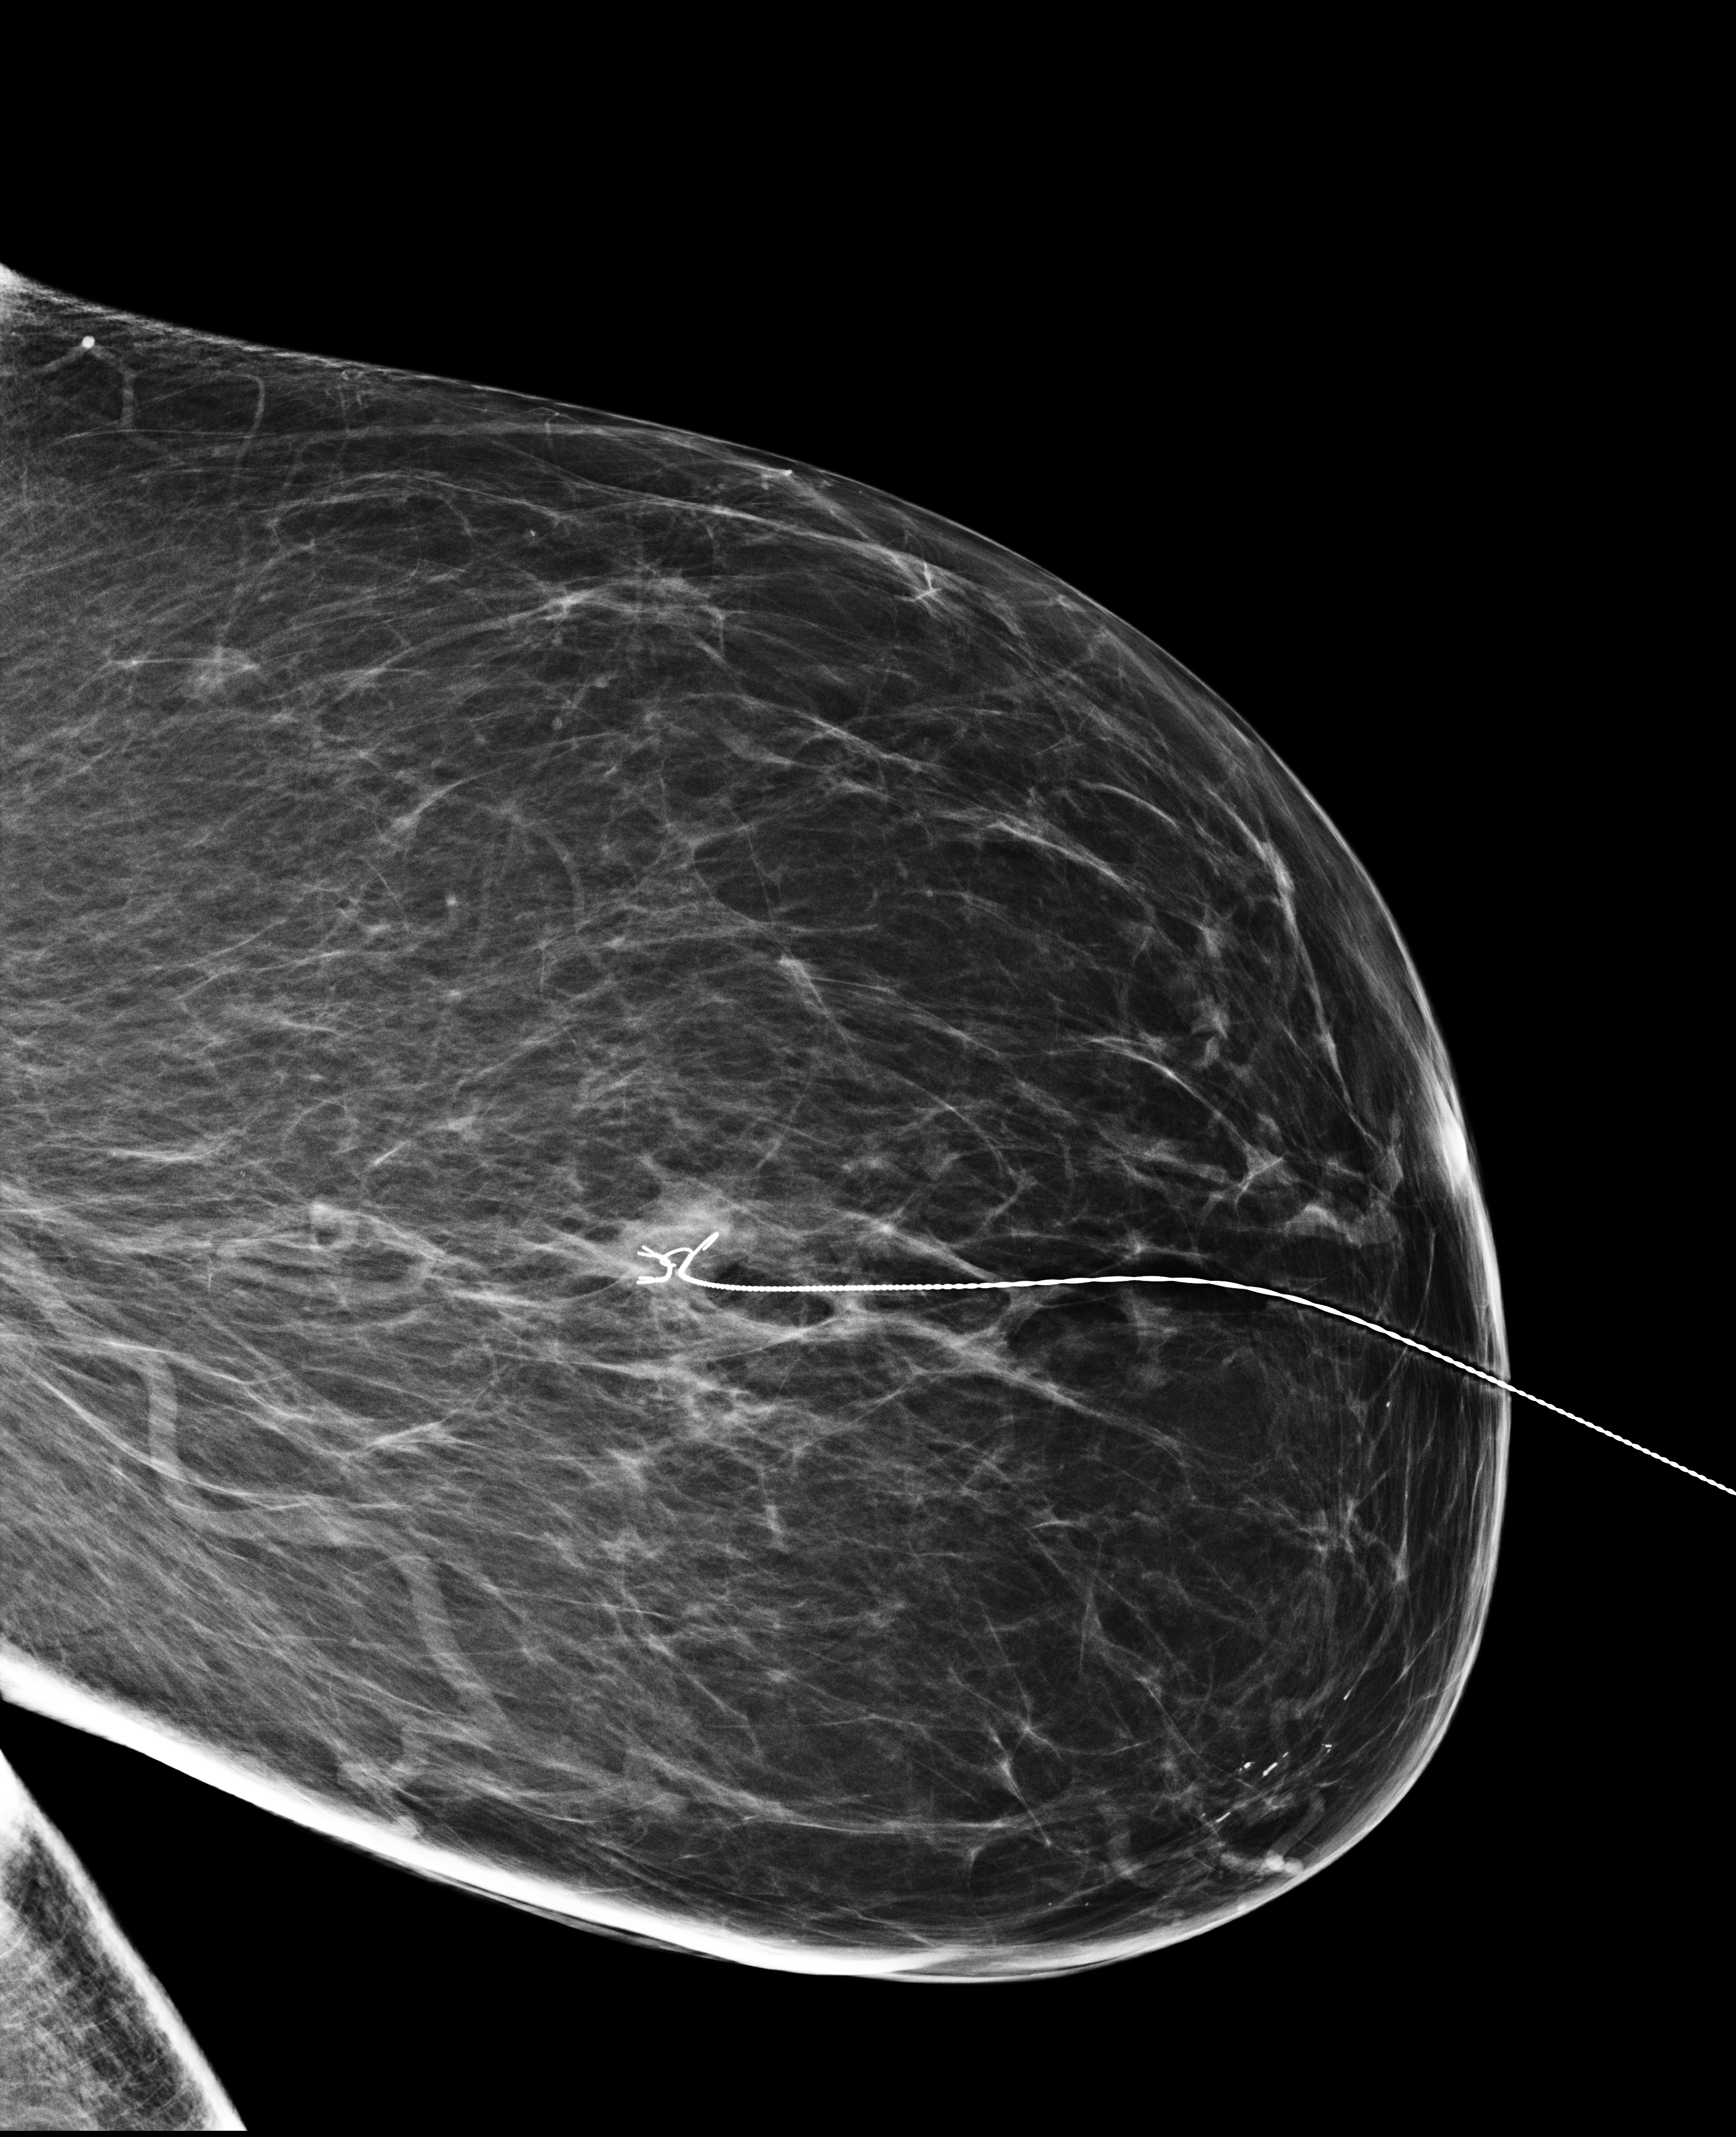
Diagnostic examination (additional views); compressed breast thickness 68 mm. Female patient, age 60 years.
Image type: full-field digital mammogram. Breast: left. Projection: ML view.